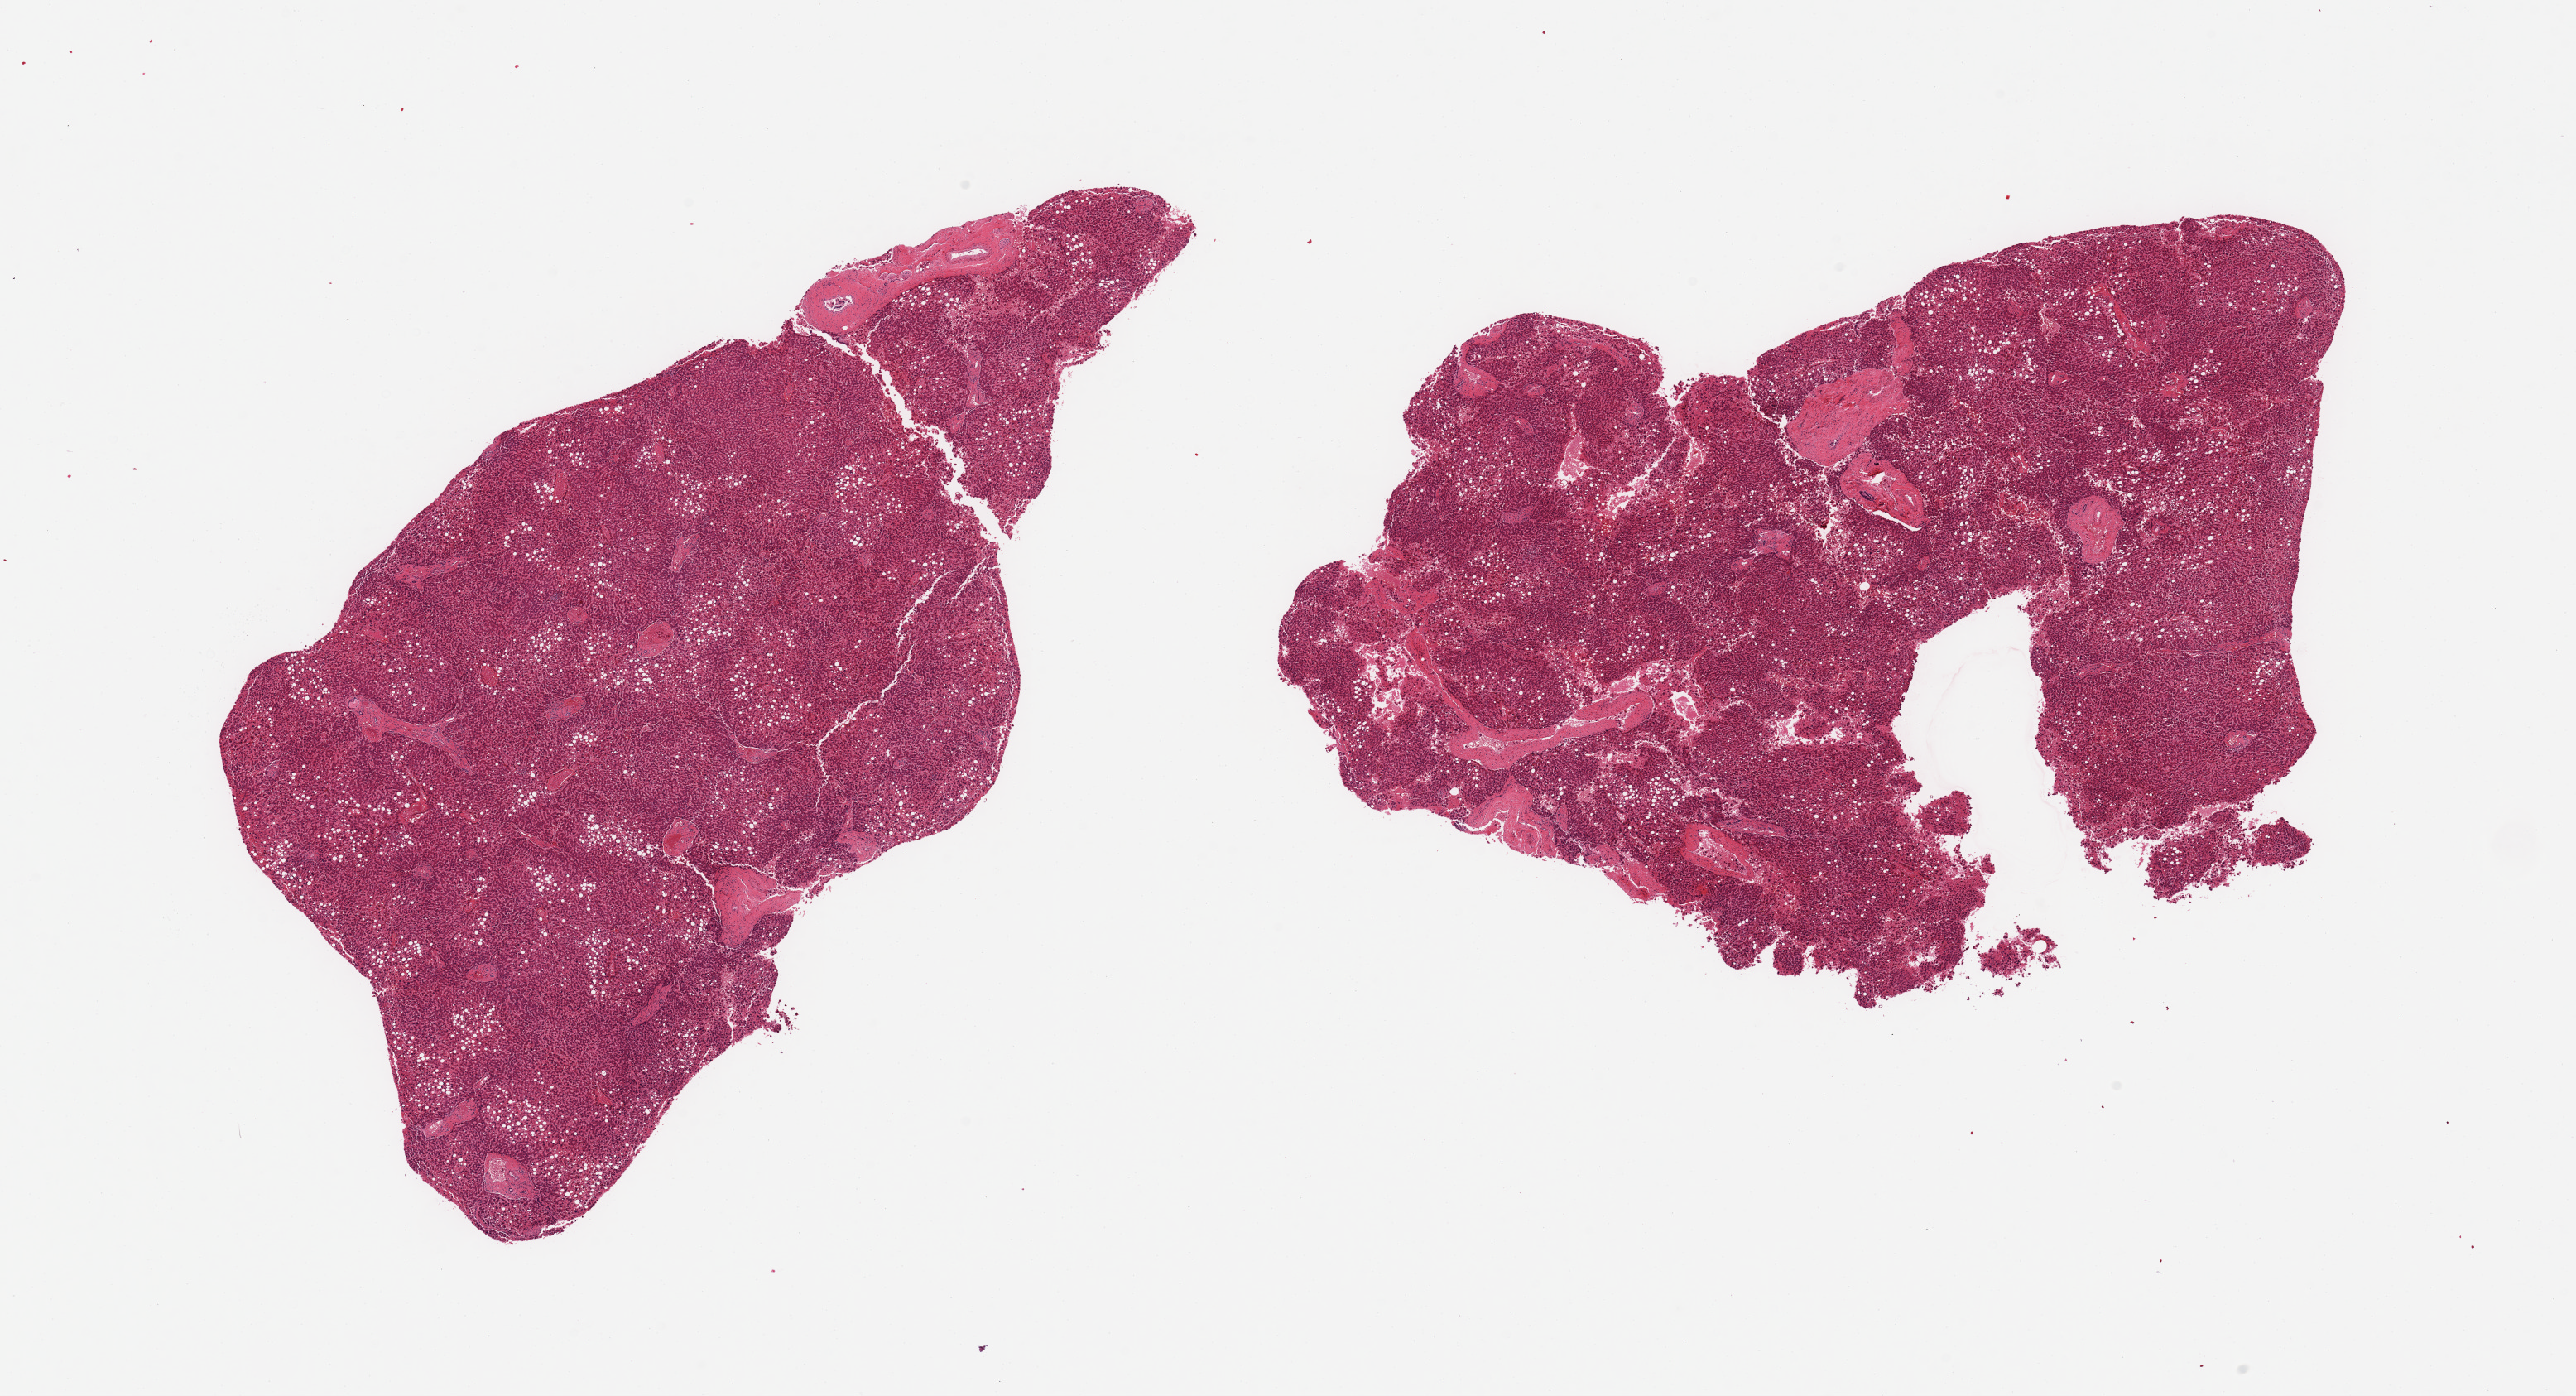
Whole-slide image, haematoxylin and eosin stain — whole scanned area (about 24.6 x 13.3 mm, slide scanned at 20x) shown as a low-resolution overview. PAXgene-fixed paraffin-embedded (PFPE) section. Section of liver (target tissue). Donor tissue sample. Donor: male.
Pathologist's review note for this sample: 2 pieces; congestion, mild to moderate steatosis.